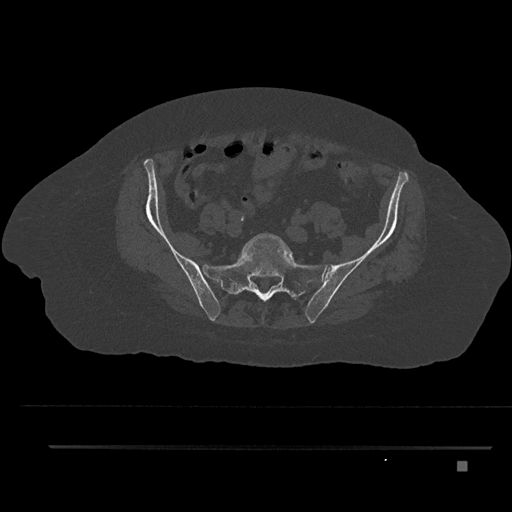
CT including the spine, one axial slice; reconstruction kernel Br40s/3; 120 kVp; bone window (W 1800 / L 400 HU); 512 × 512 image matrix, field of view 437 × 437 mm. Patient: female, 76 years. From the clinical record (not read from this slice): primary cancer: lung; vertebrae with lytic lesions (as recorded): T11, L3.
Annotated regions visible in this slice (semi-automatic segmentation, software-assisted and operator-edited):
- L5 vertebra: box from (x=243, y=233) to (x=293, y=295) px